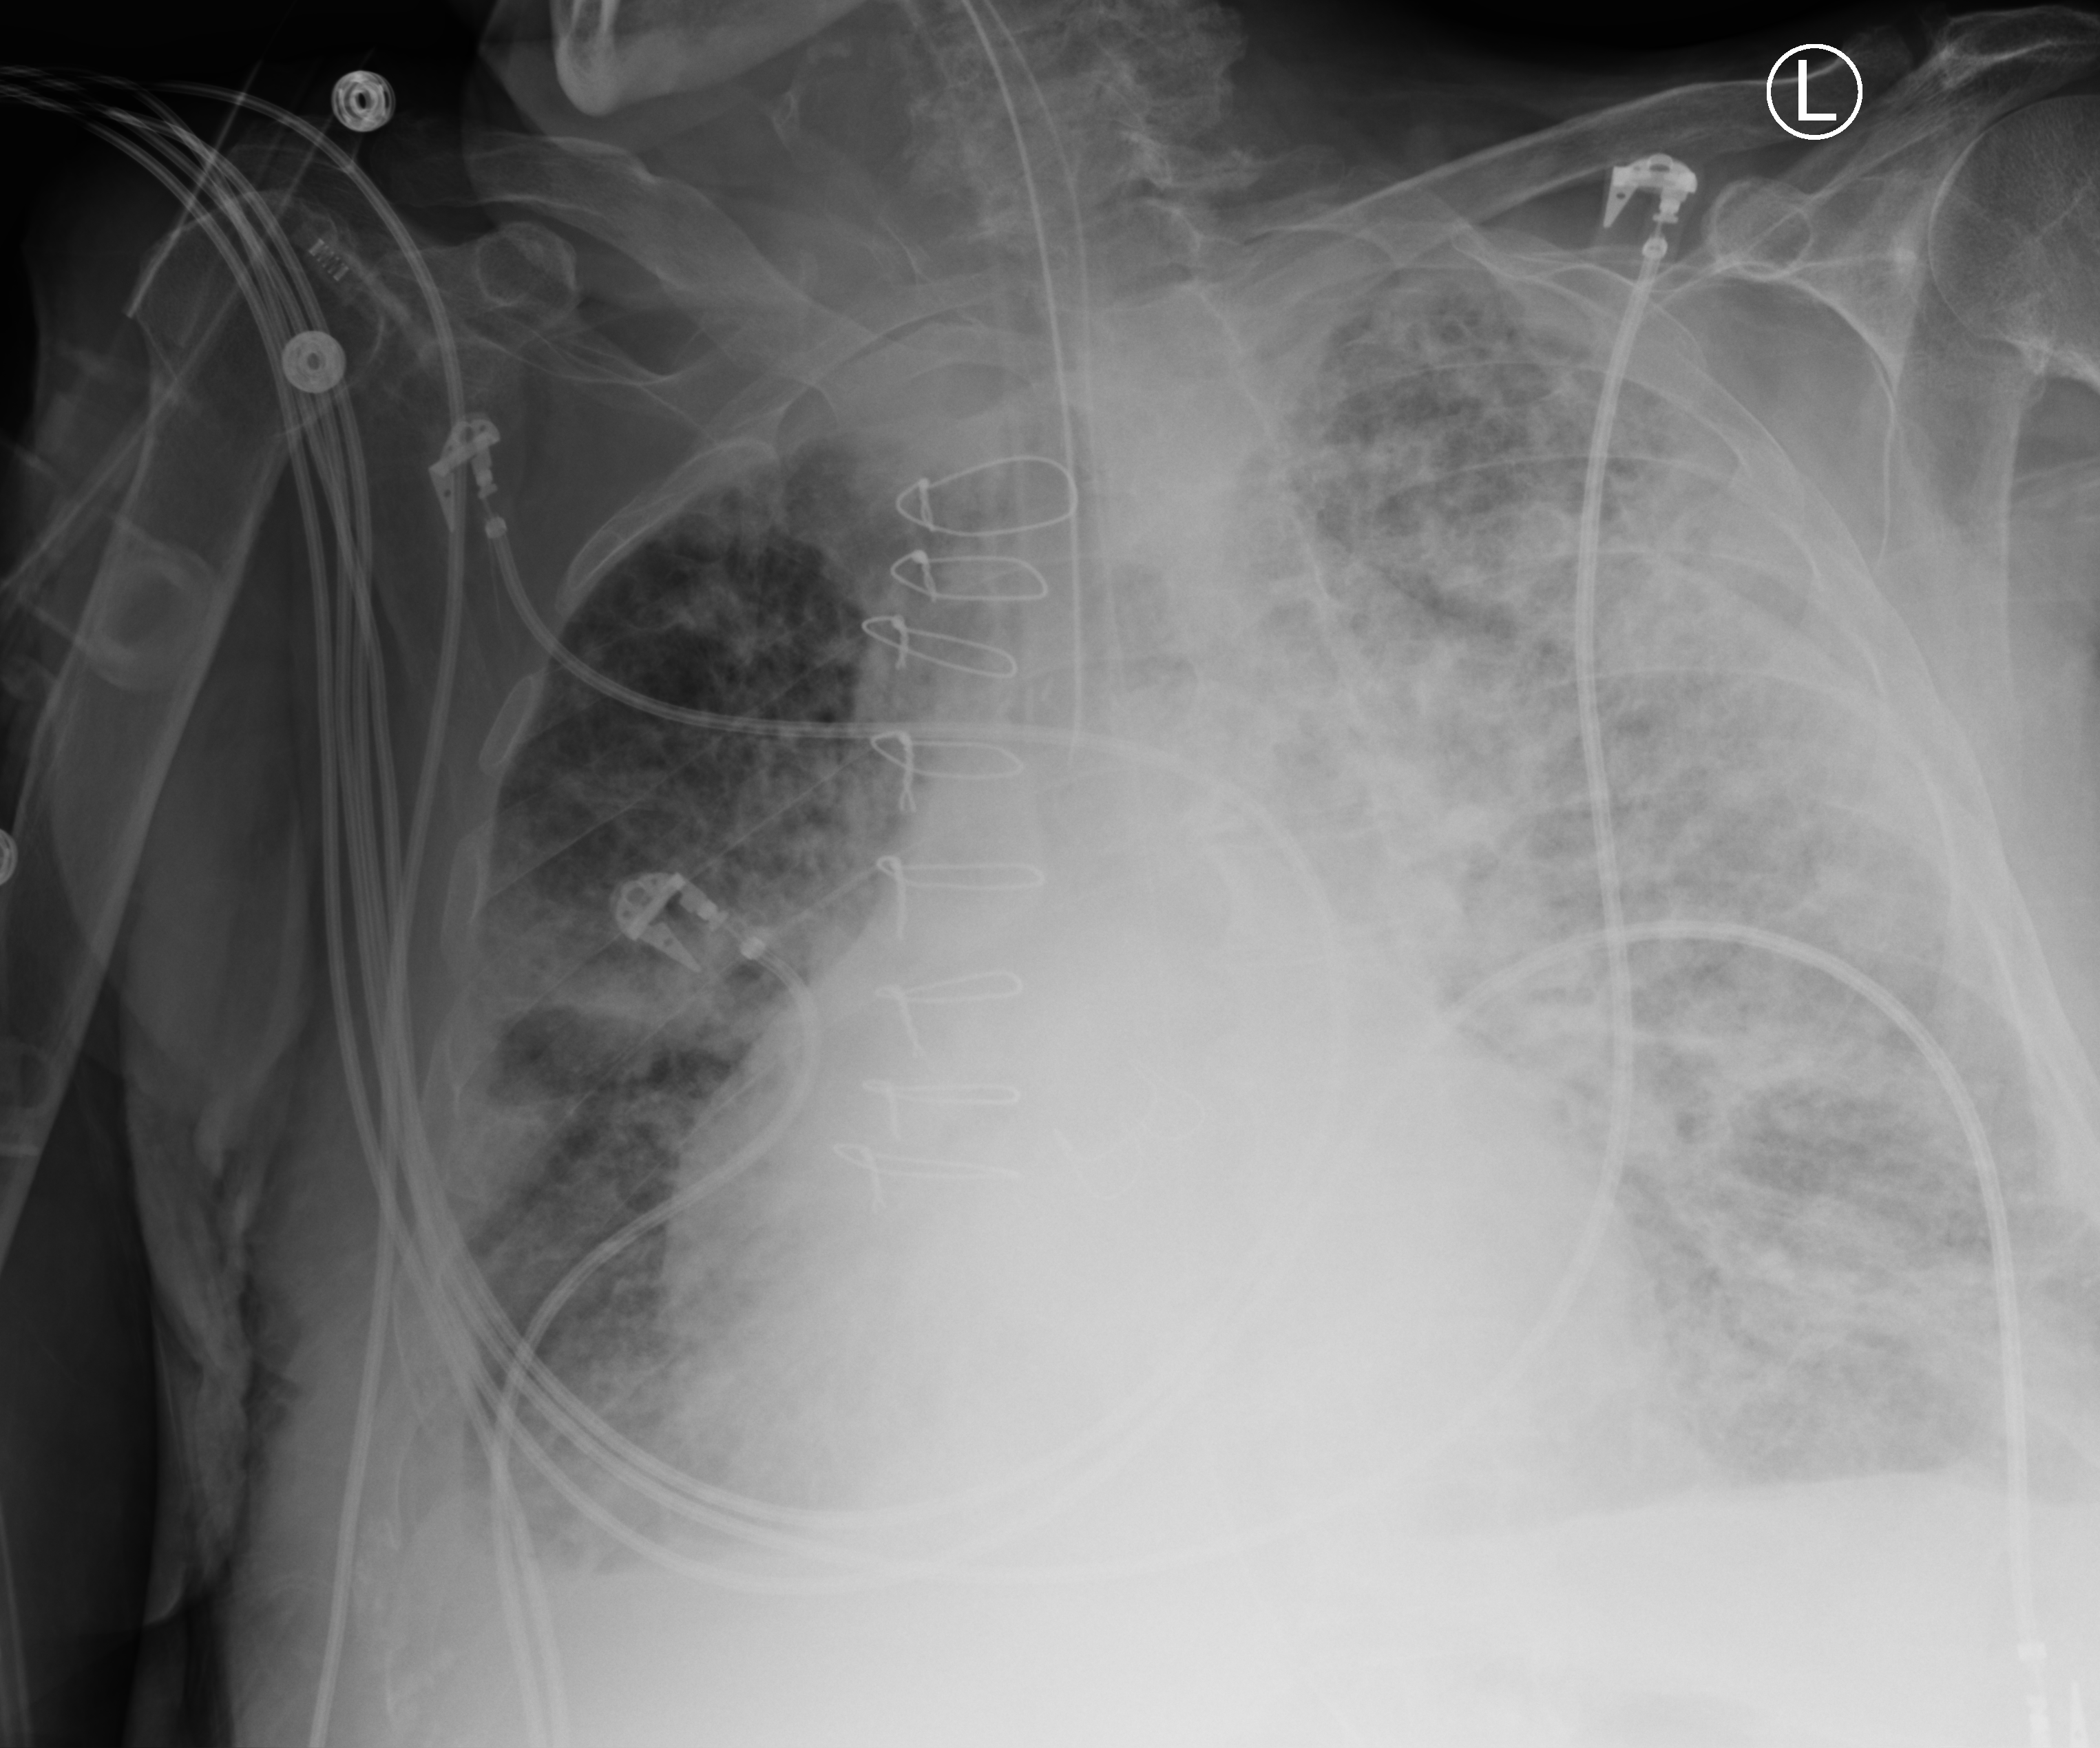
Portable chest radiograph; anteroposterior (AP) projection. Male patient hospitalised with COVID-19, age 75–90 years.
Hospital-stay facts (about this admission, not read from this image; timing relative to this image not recorded):
- admitted to intensive care during this hospital stay: yes
- mechanically ventilated during this hospital stay: yes